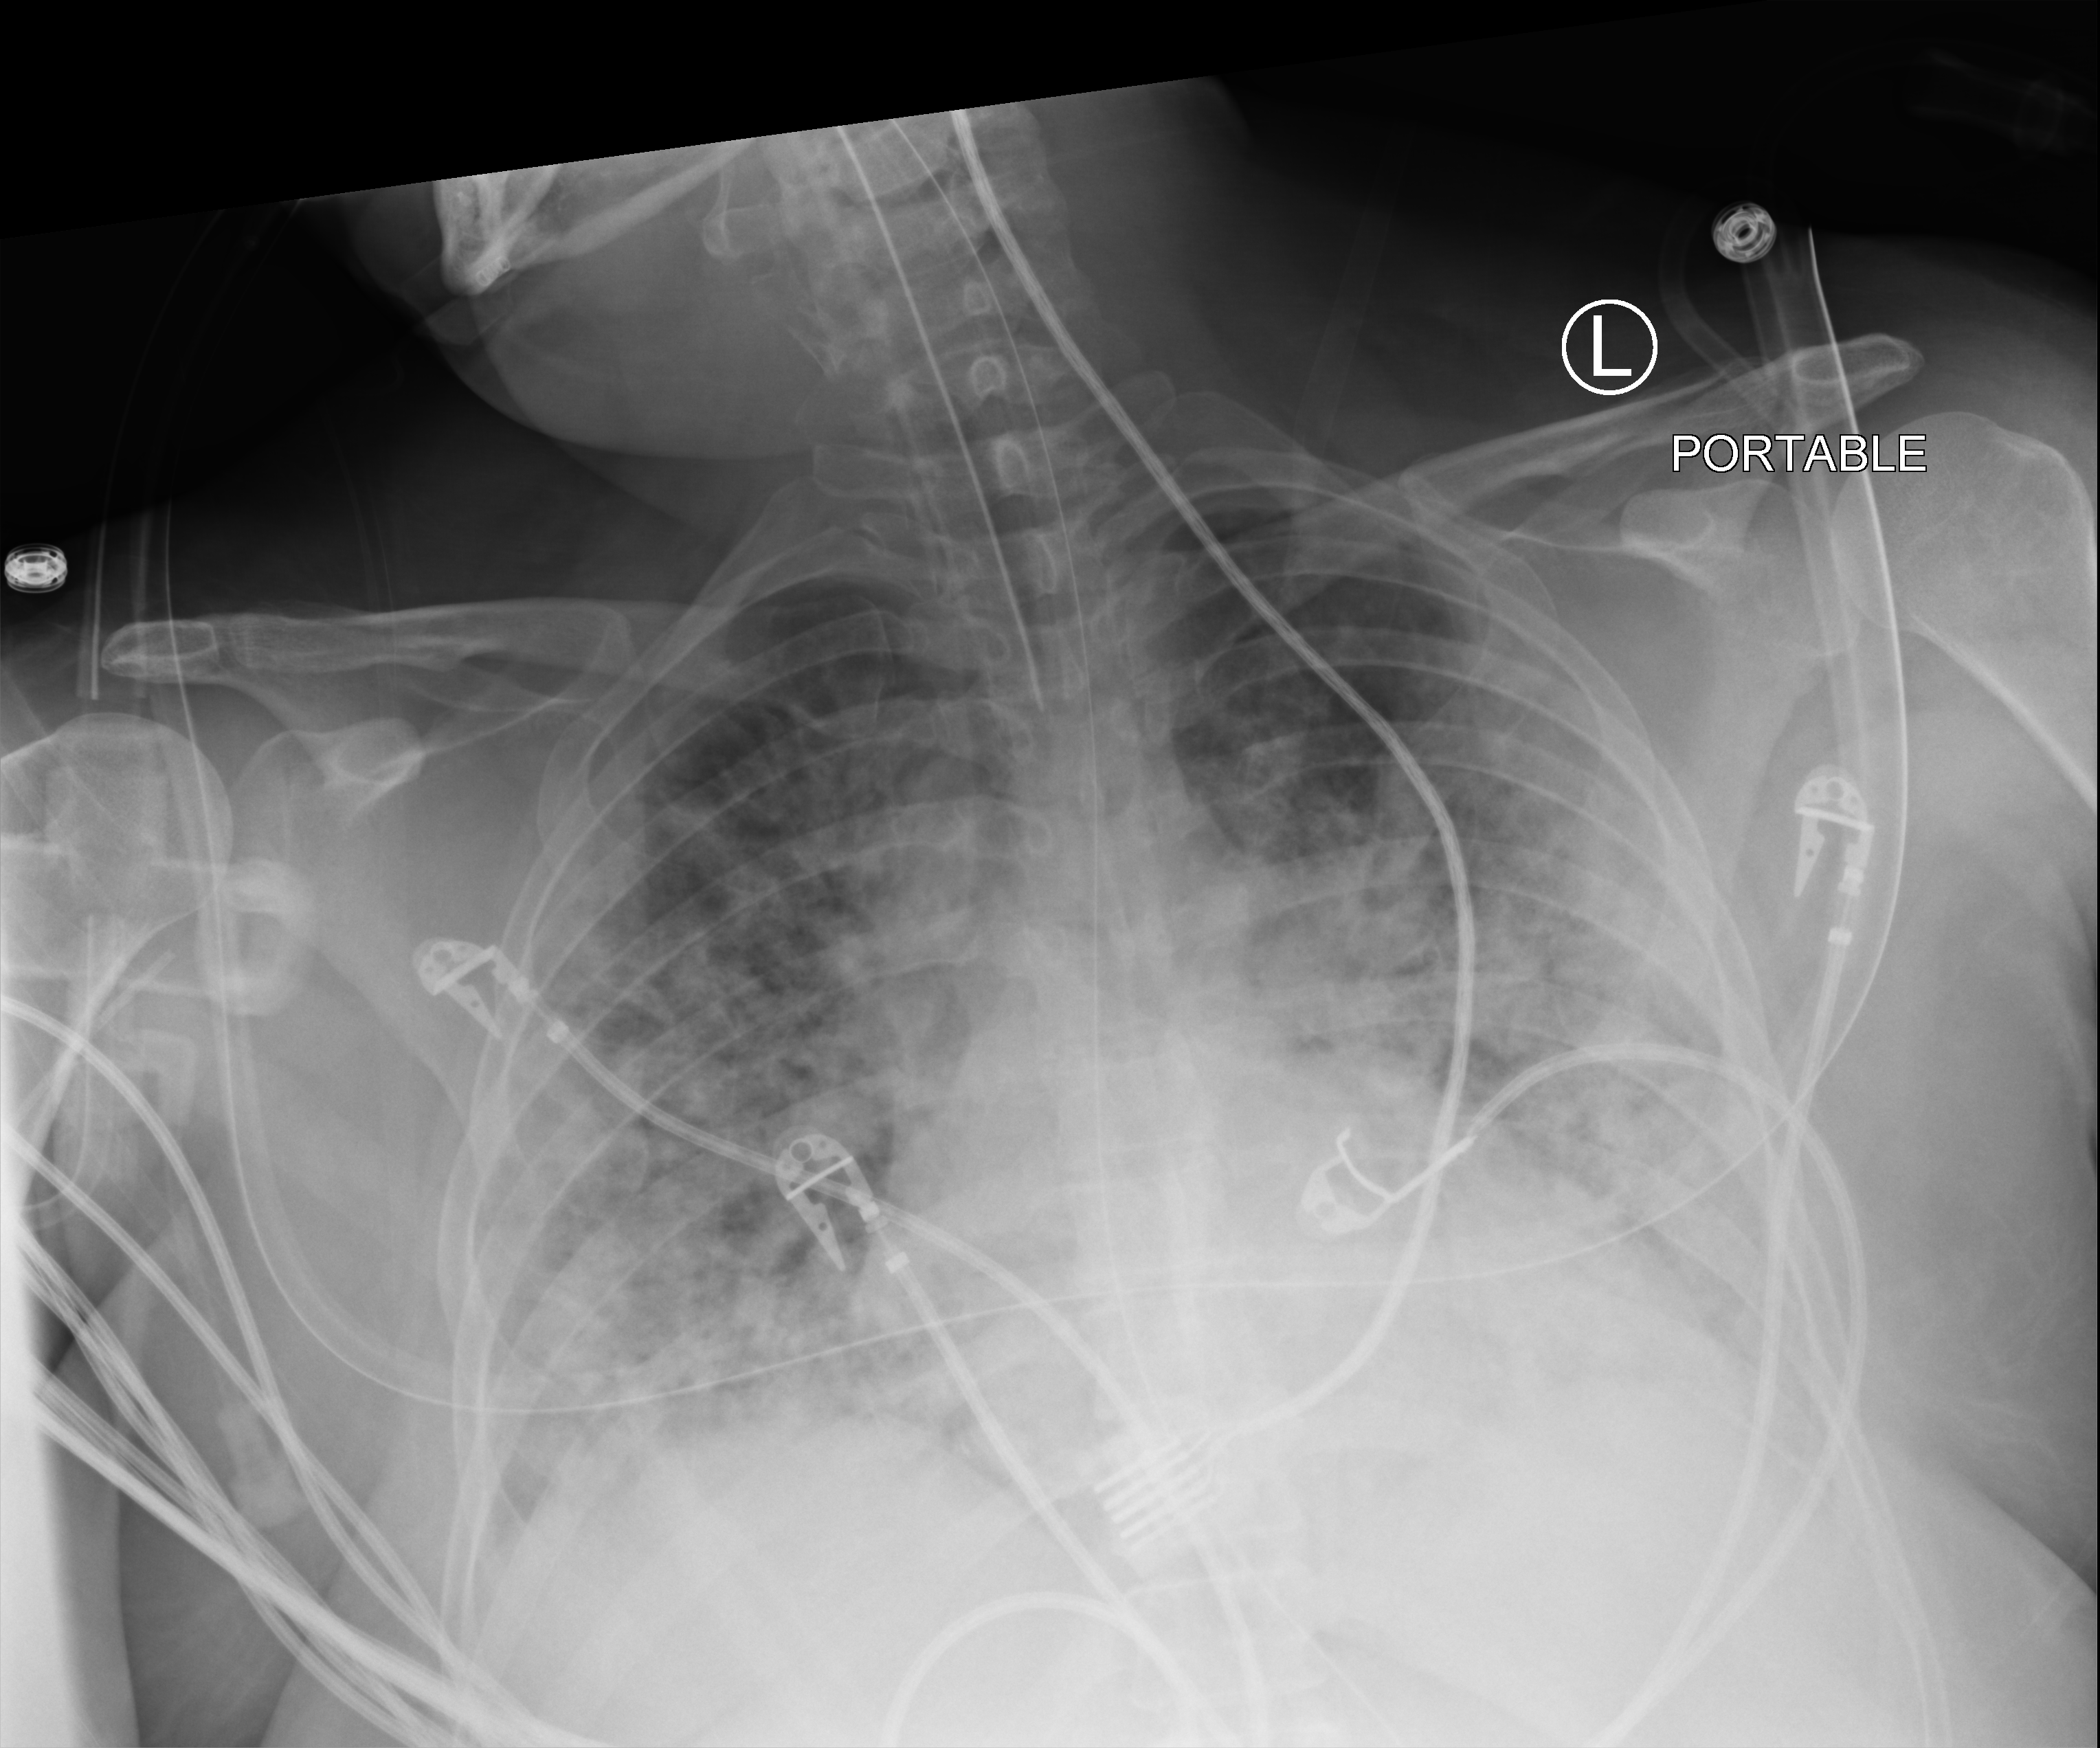
Chest X-ray (portable). Patient hospitalised with COVID-19; female, aged 18–59 years.
From the hospital-stay record, not from the radiograph (when in the stay this image was taken is not recorded):
- admitted to intensive care during this hospital stay: yes
- mechanically ventilated during this hospital stay: yes